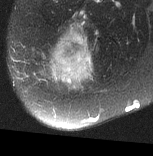
MRI of an extremity soft-tissue mass, one axial slice. T2-weighted fat-saturated. MR volume resampled by the dataset authors to the PET/CT grid (not the native acquisition matrix). 3.27 mm slice thickness. 153 × 156 image matrix. Female patient. Case-level facts recorded for this patient, not image findings: histological type: synovial sarcoma; grade: intermediate; site of the primary tumour: right buttock.
Outlined on this slice (expert contour drawn on MRI and transferred to this co-registered scan by the dataset authors):
- gross tumour volume including surrounding oedema: bounding box <42,22,95,91> (left, top, right, bottom; pixels)
- gross tumour volume (mass): <44,31,95,87>